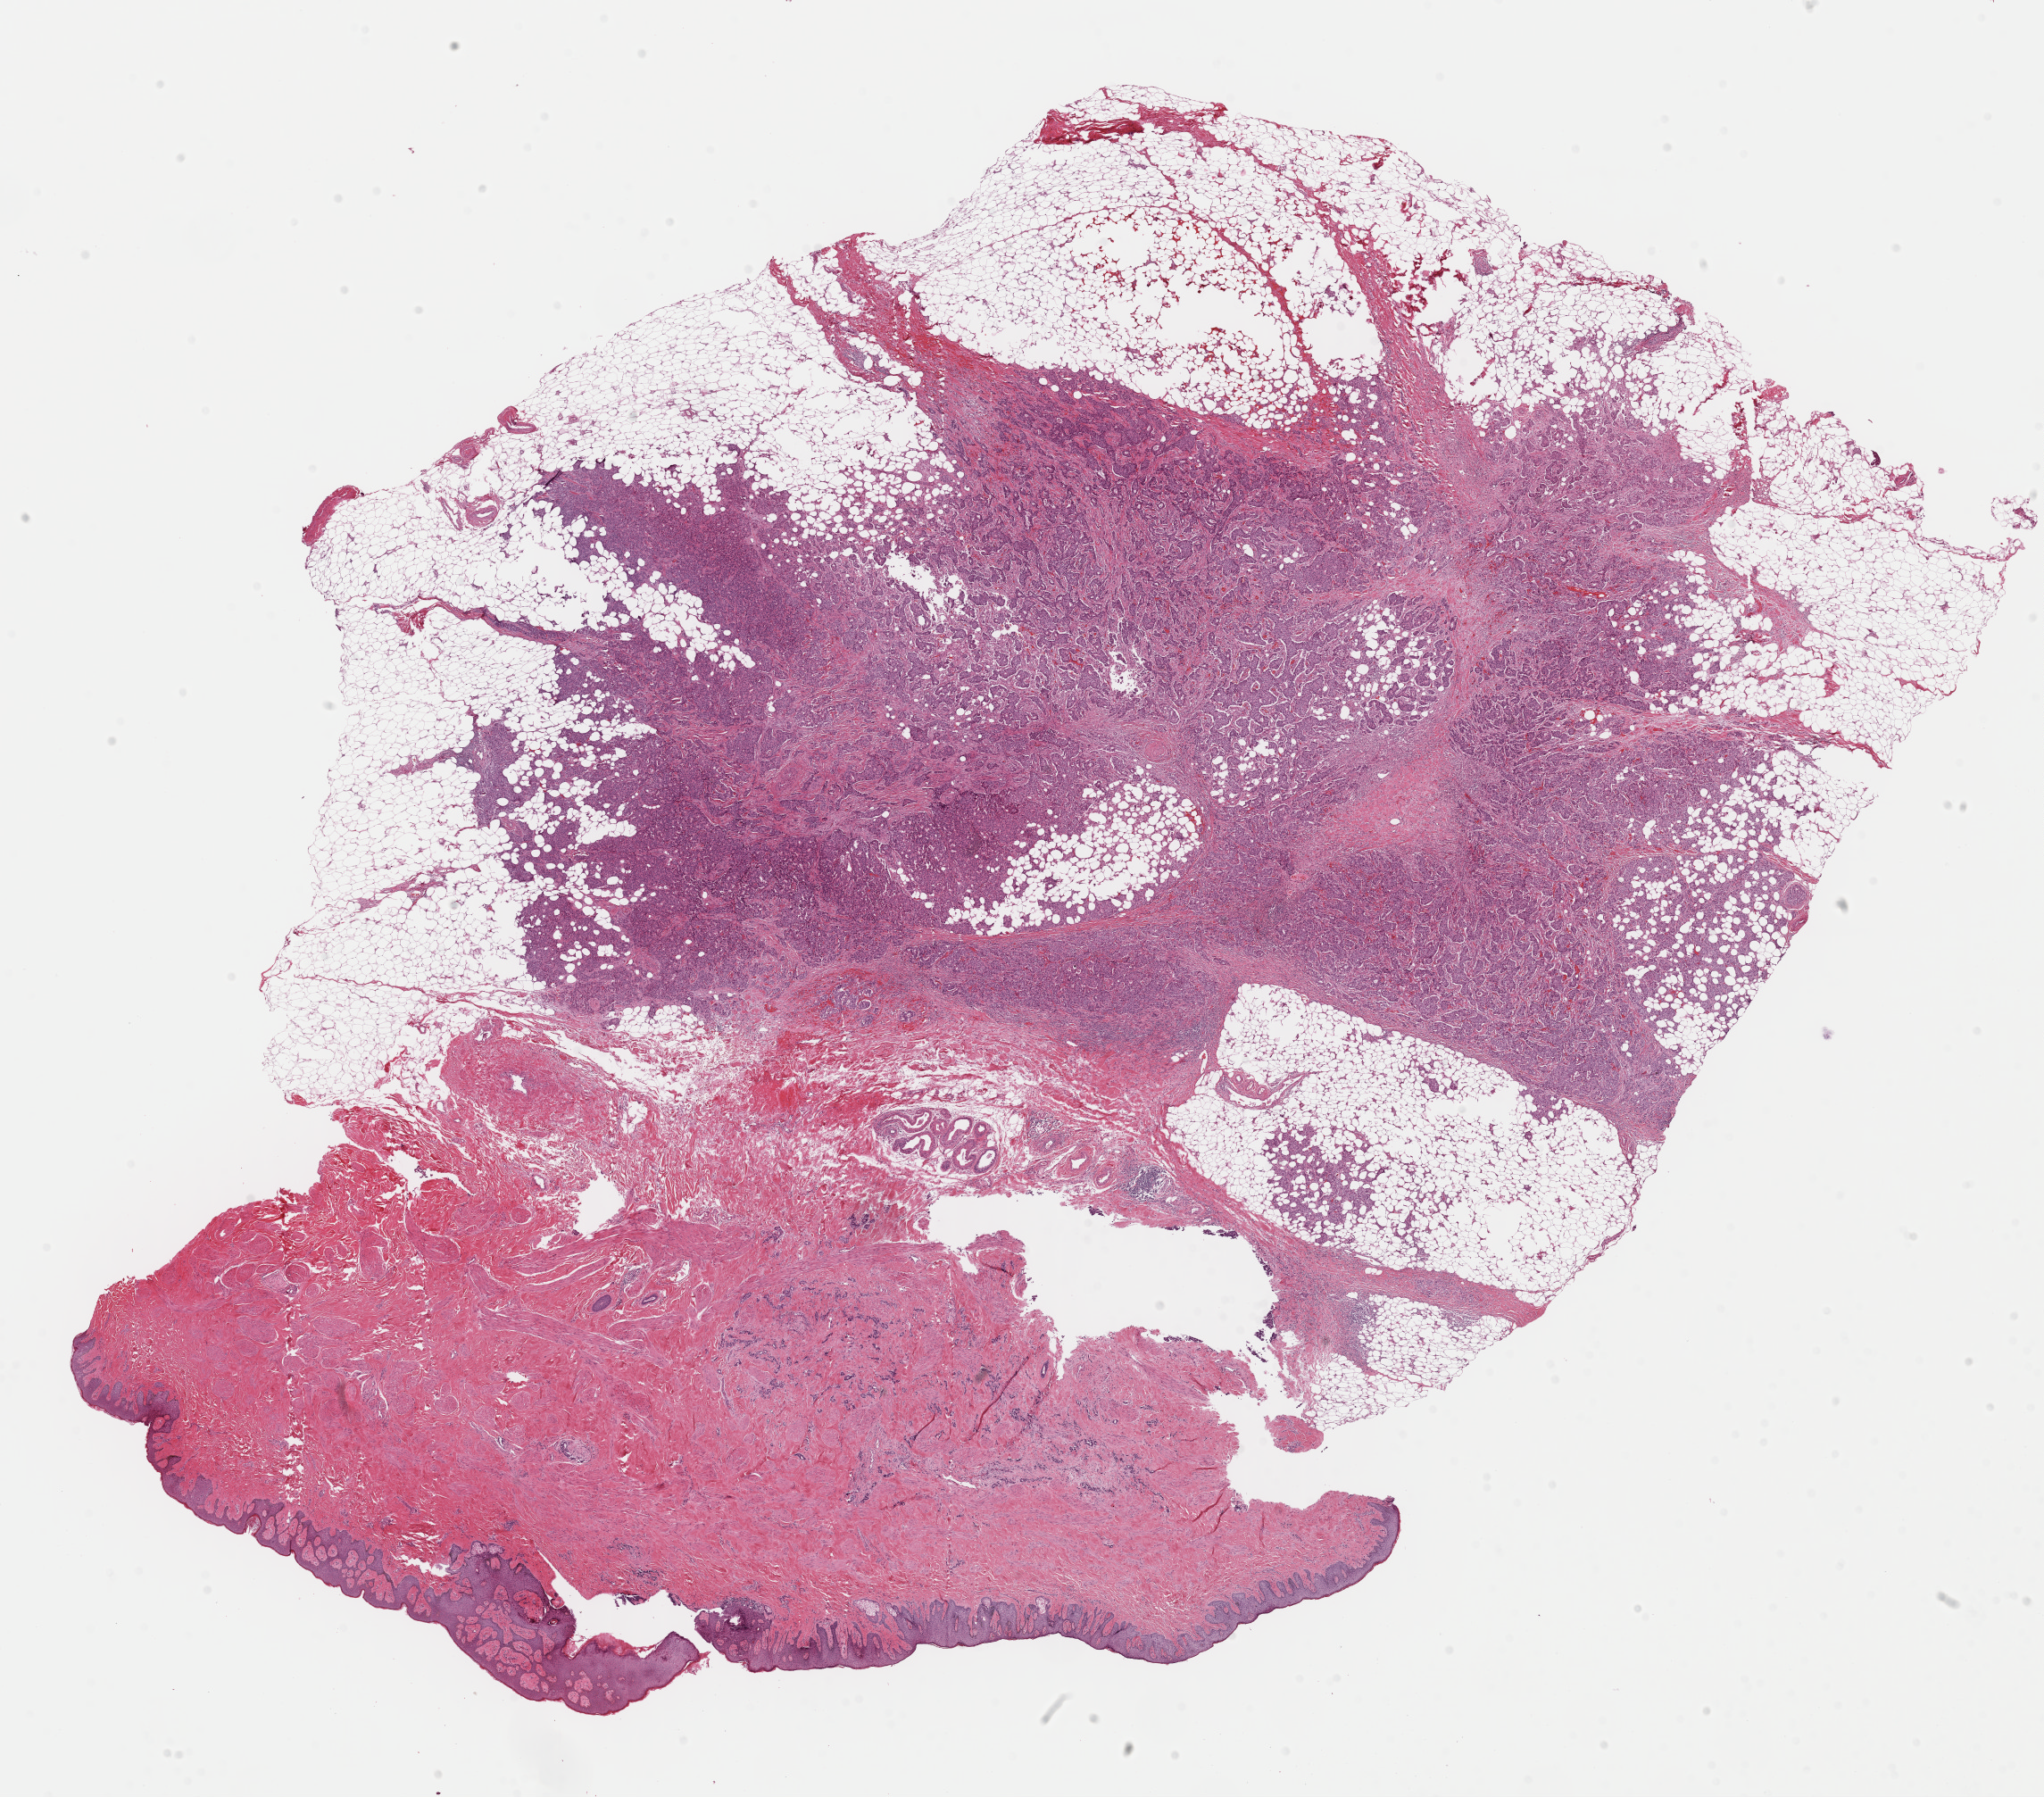
Whole-slide histology image, Hematoxylin and eosin (H&E) stained — low-resolution overview of the scanned area, about 18.1 x 15.9 mm (from a 40x scan), FFPE section, breast, primary tumour sample. Patient: male, age at initial diagnosis 68 years.
Histologic diagnosis: Infiltrating duct carcinoma, NOS. Lymph nodes positive (case pathology): 1 of 25 examined. AJCC pathologic stage: IIB (6th edition).